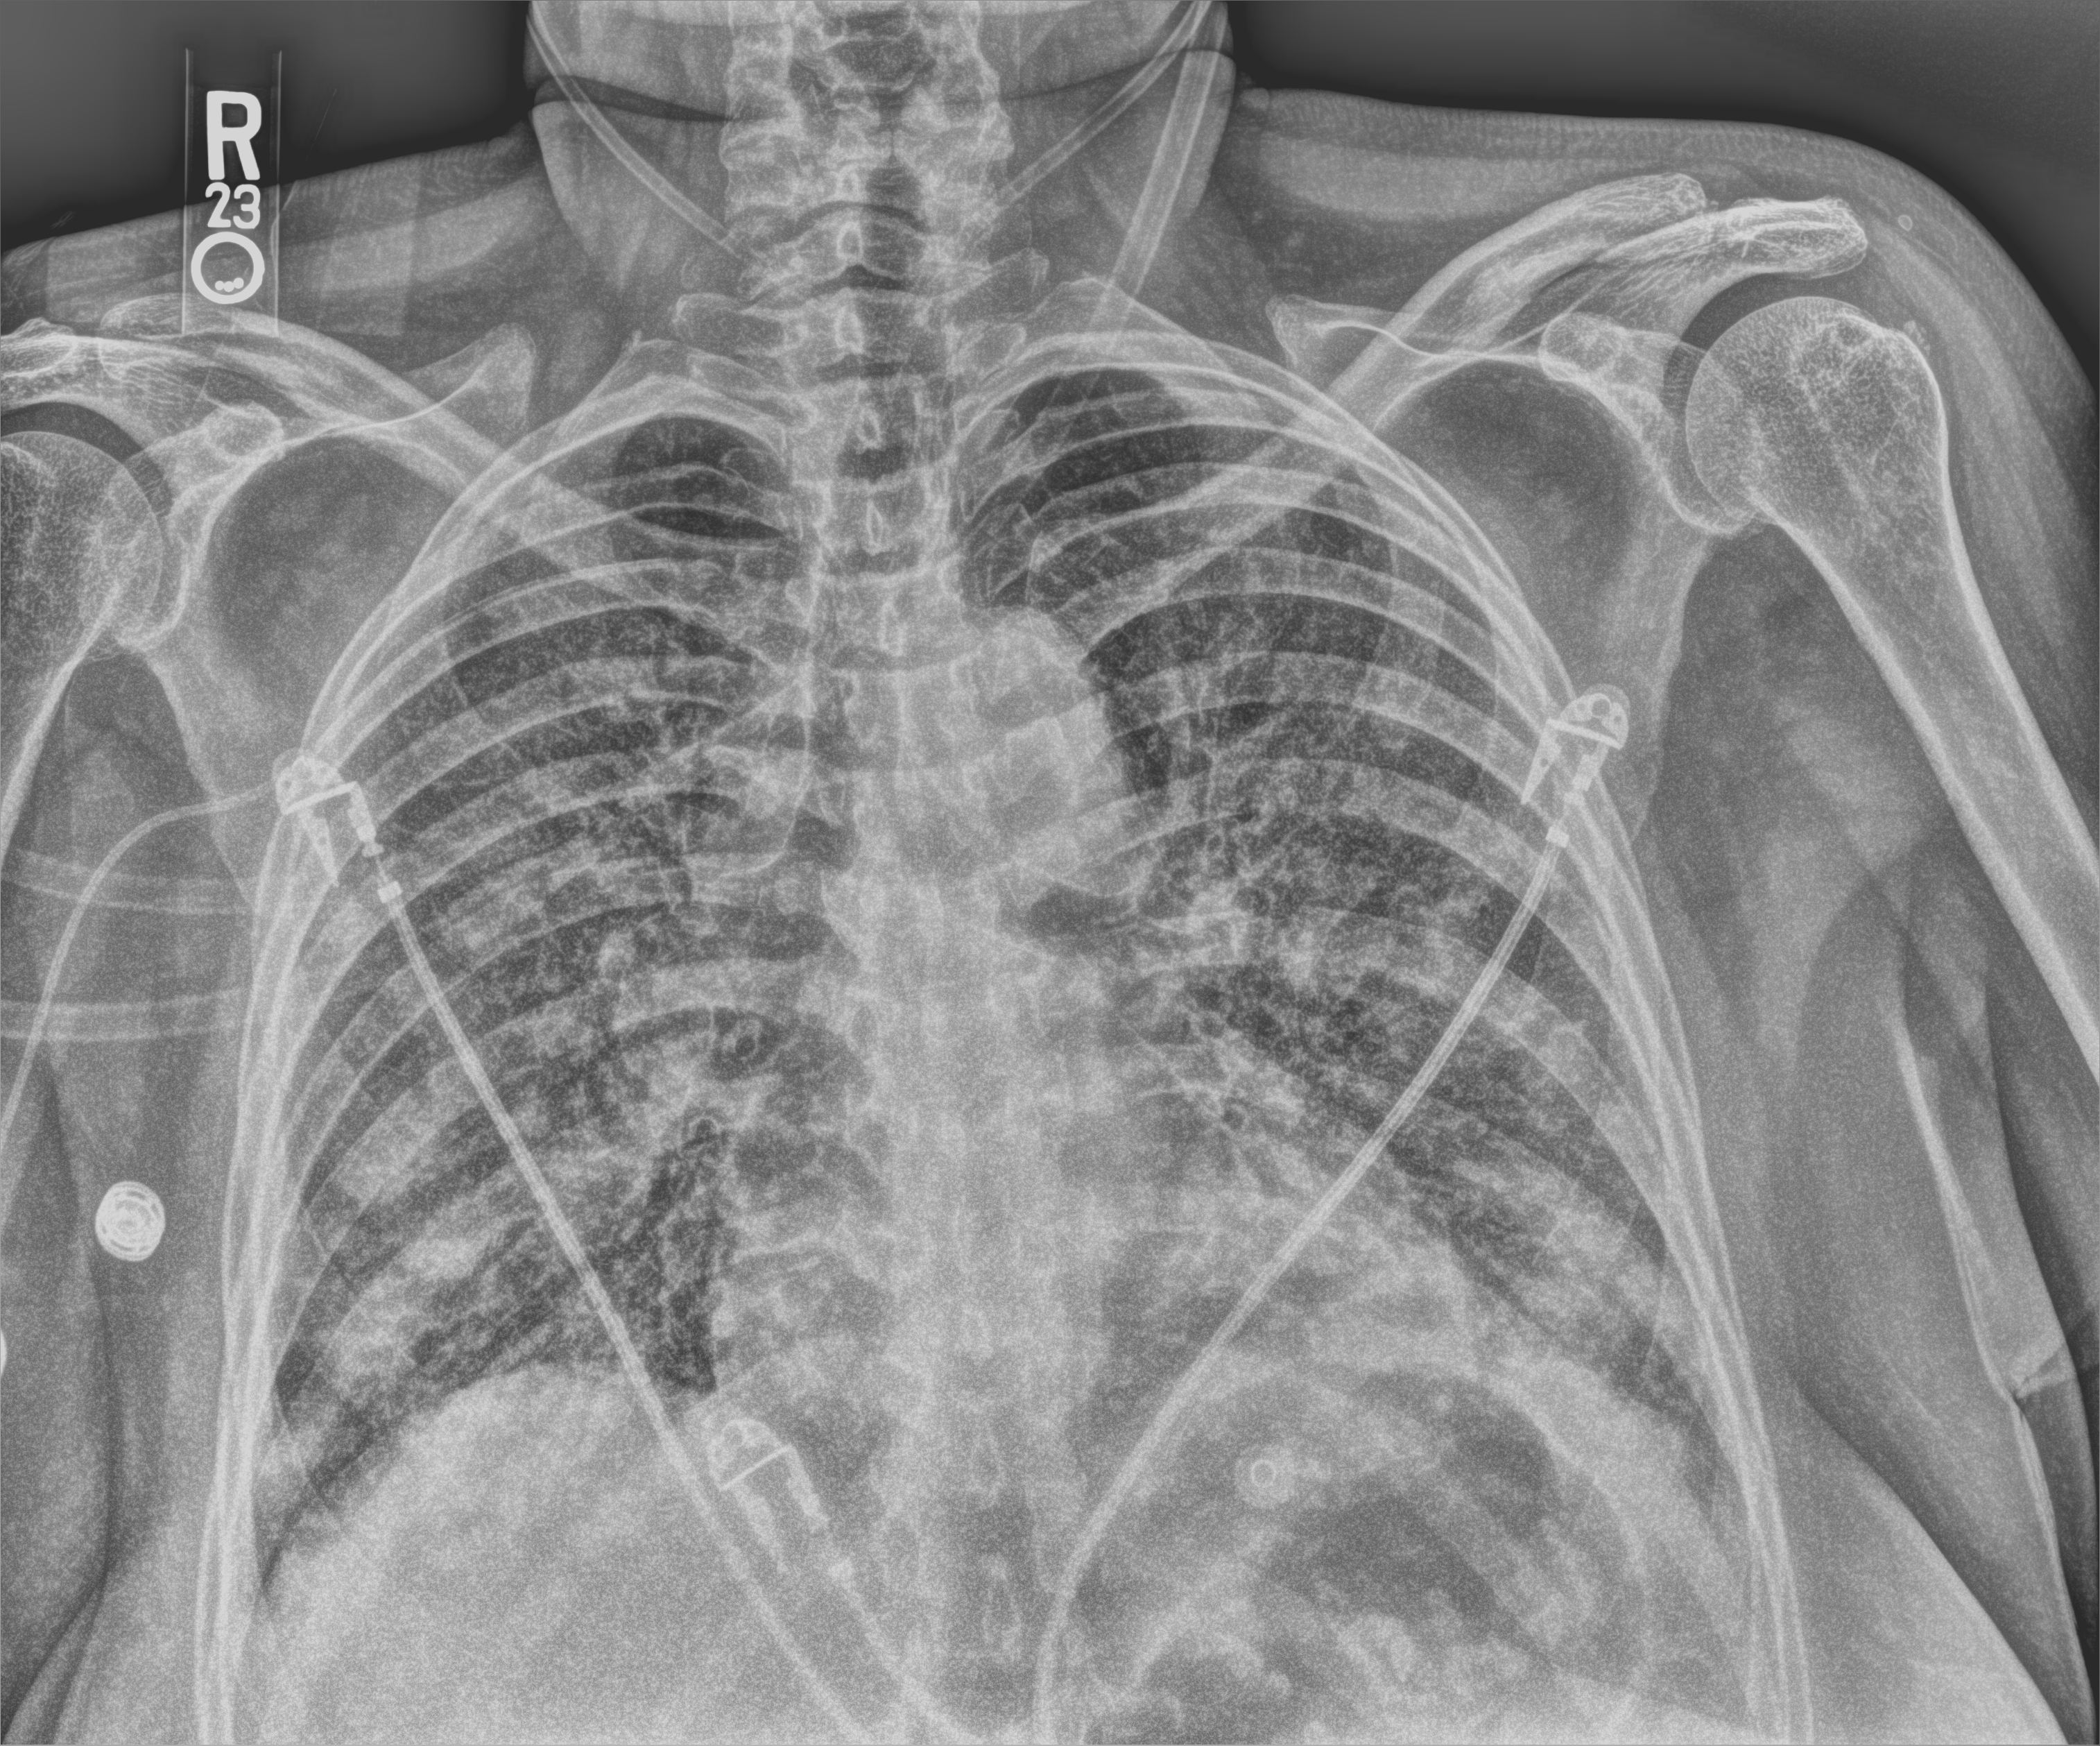
Chest X-ray (portable); anteroposterior (AP) projection. Patient hospitalised with COVID-19; female, aged 75–90 years.
Admission-level facts for this patient (not findings on this image; timing relative to this image not recorded):
- admitted to intensive care during this hospital stay: yes
- mechanically ventilated during this hospital stay: yes